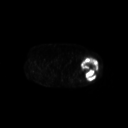
FDG PET of an extremity soft-tissue mass (from a PET/CT study), one axial slice; slice 235 of 267 in the series (ordered by position); 3.27 mm slice thickness; 128 × 128 image matrix. Patient: female, 62 years. Case-level facts recorded for this patient, not image findings: histological type: undifferentiated – high grade; grade: high; site of the primary tumour: left thigh.
Structures marked on this image (expert contour drawn on MRI and transferred to this co-registered scan by the dataset authors):
- gross tumour volume including surrounding oedema: bounding box [x1, y1, x2, y2] px = [81, 57, 99, 81]
- gross tumour volume (mass): [81, 57, 98, 81]